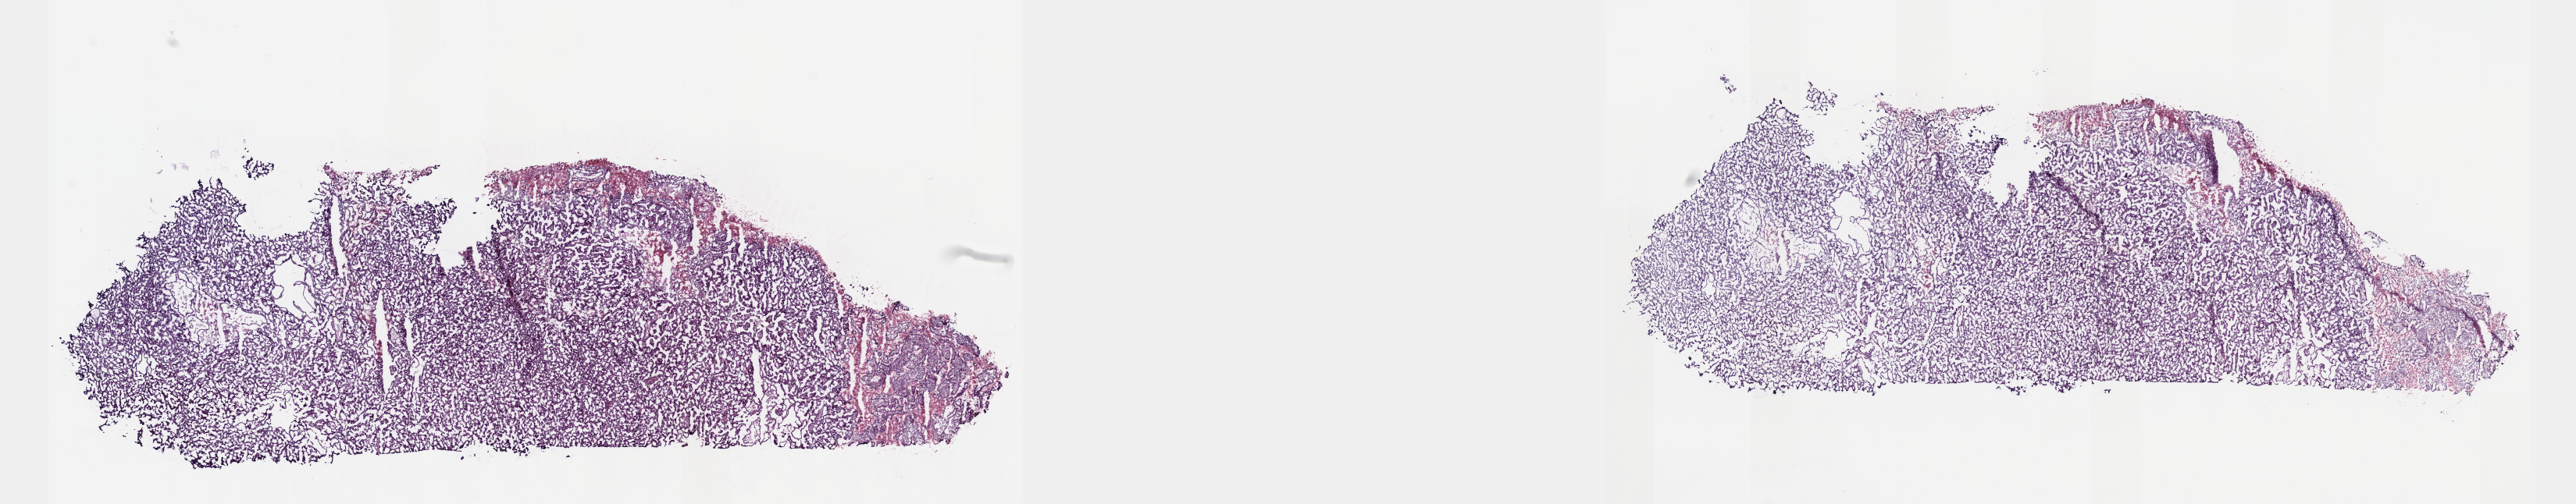
Whole-slide histology image, Hematoxylin and eosin (H&E) stained — a low-resolution overview of the entire scanned area, about 26.7 x 5.2 mm (acquisition: 40x scan), frozen section, primary tumour sample from the kidney. Male patient; age at initial diagnosis 60 years. Pathologist review of this section (percent, as recorded): tumour cells 100%, tumour nuclei 95%, normal cells 0%, stromal cells 0%, necrosis 0%. Infiltration values recorded for this section: lymphocyte infiltration 0%, monocyte infiltration 0%, neutrophil infiltration 0%.
Diagnosis: Papillary adenocarcinoma, NOS. TNM: T1 NX MX. Laterality: left. AJCC pathologic stage: I.